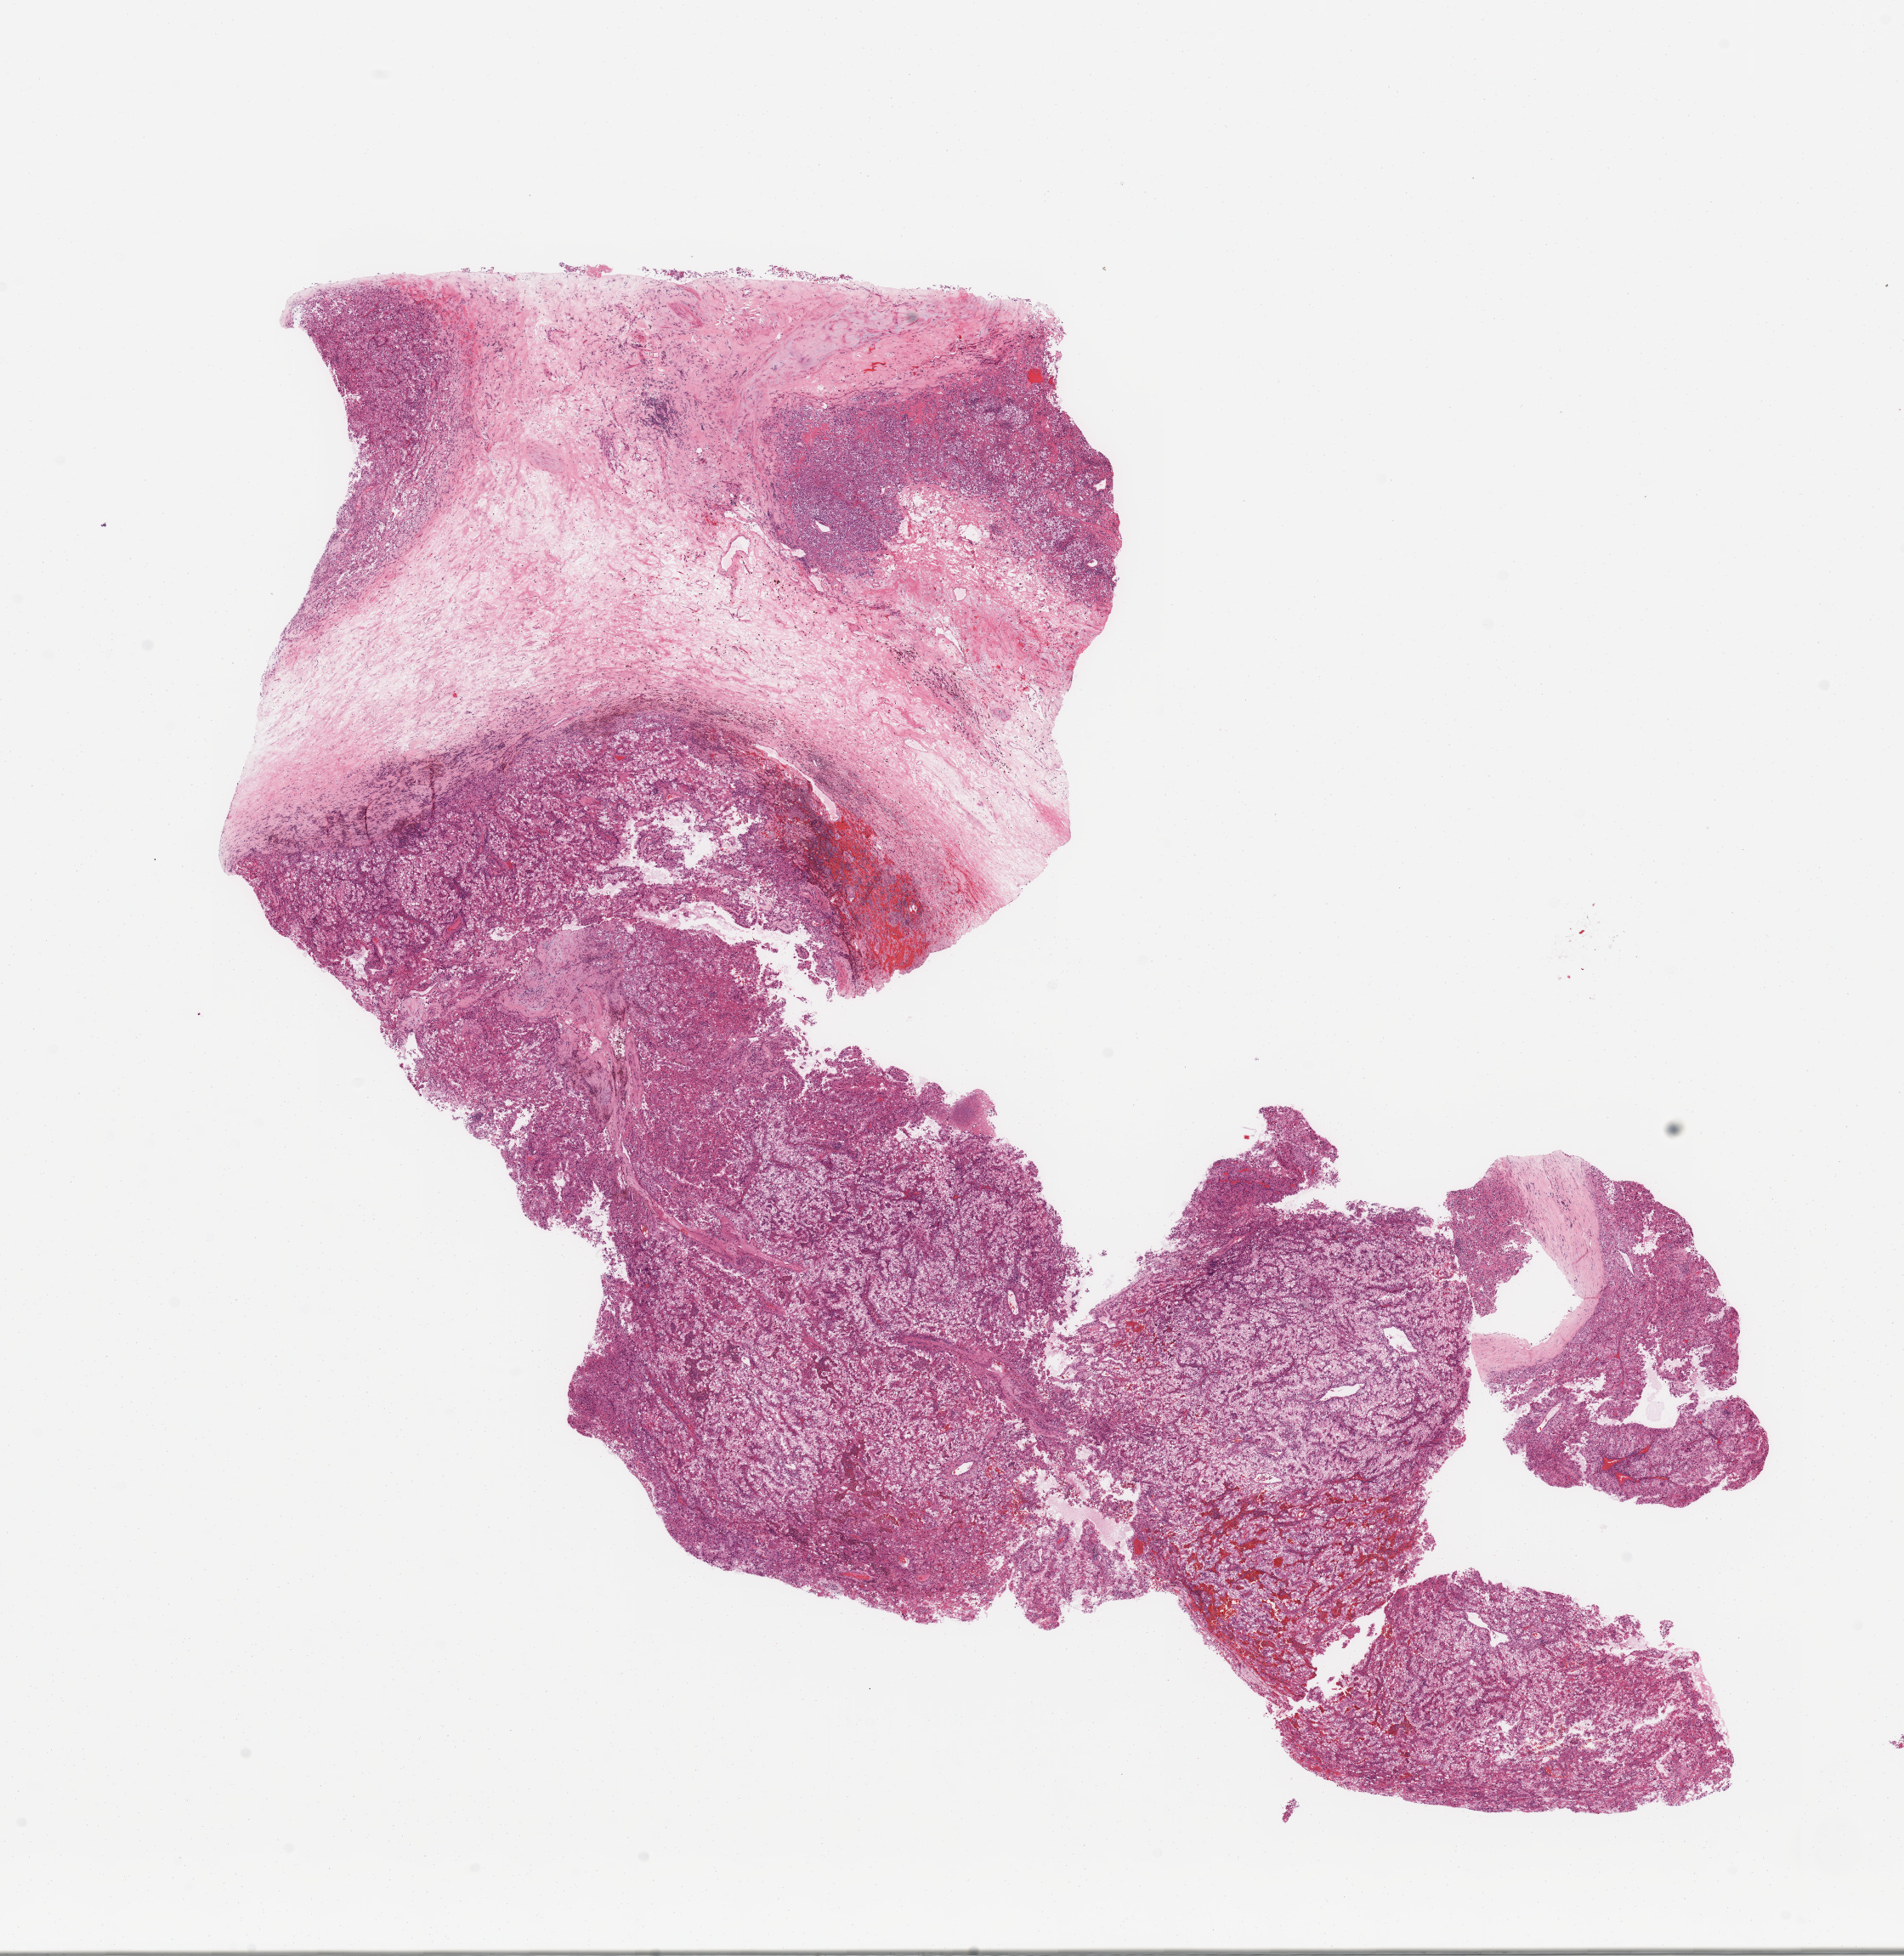
Digitized H&E-stained tissue section (whole slide), whole scanned area (about 17.7 x 18.2 mm, slide scanned at 20x) shown as a low-resolution overview, tumour tissue sample, sampled site: kidney. 50-year-old male patient. Histologic grade: G4 (undifferentiated). Pathologist review of this section (percent, as recorded): tumour nuclei 90%, necrosis 5%.
- diagnosis: Renal cell carcinoma, NOS
- AJCC pathologic stage: III
- primary tumour site (as recorded): middle